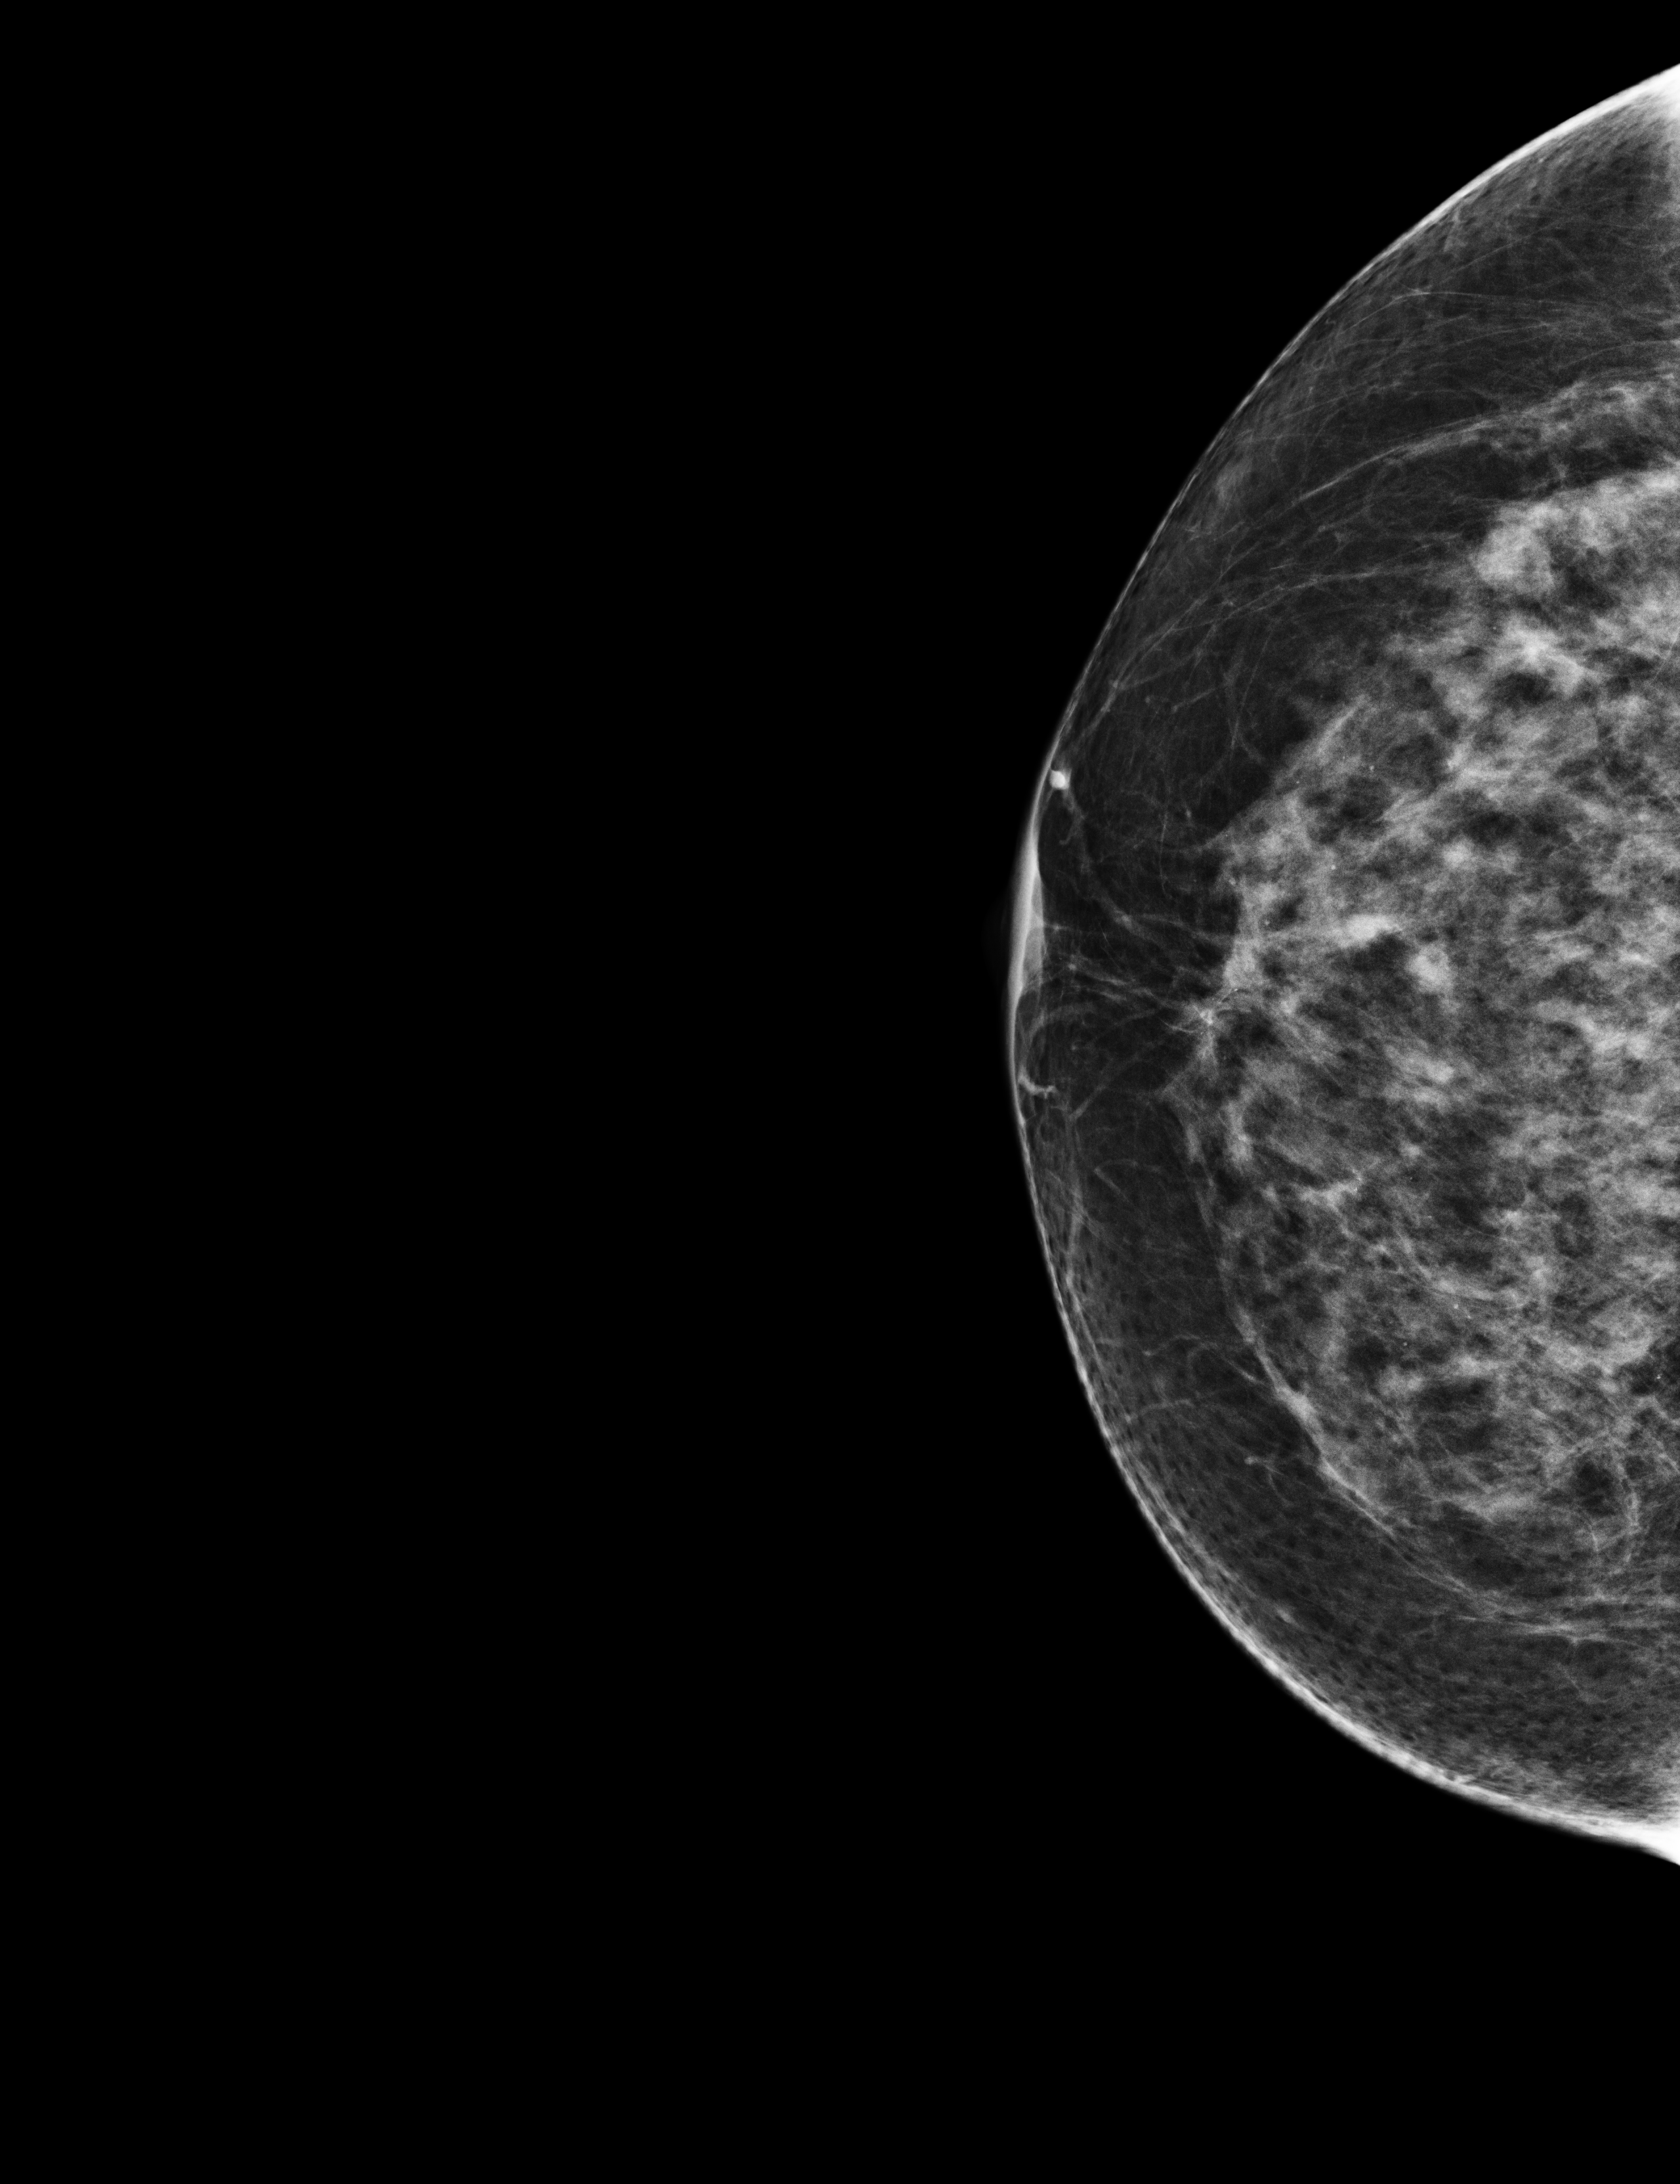
Digital mammogram (FFDM); right breast; cranio-caudal projection; screening examination. Patient: female, 70 years.
Final BI-RADS category for the screening round (tomosynthesis exam, both breasts): category 2.